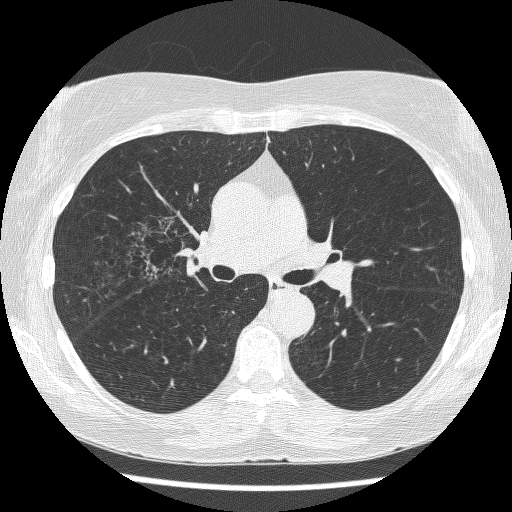
Chest CT (low-dose screening protocol), one axial image, baseline screening round, lung window (W 1500 / L -600 HU), 1.25 mm slice thickness, lung (sharp) reconstruction kernel (BONE), 120 kVp, 512 × 512 image matrix. Female participant, aged 64 years at enrolment. Former smoker at enrolment.
• Expert reader's lesion annotation, bounding box [x1, y1, x2, y2] px = [123, 216, 200, 279].
• The screening reader recorded 3 non-calcified nodules or masses ≥4 mm on this exam (right upper lobe, right upper lobe, left lower lobe); which of them this box marks is not recorded.
• Lung cancer was diagnosed 735 days after this screen (after the third annual screen): adenocarcinoma, NOS, right upper lobe, right middle lobe, right hilum, stage IV (AJCC 6th edition), 85 mm at pathology.